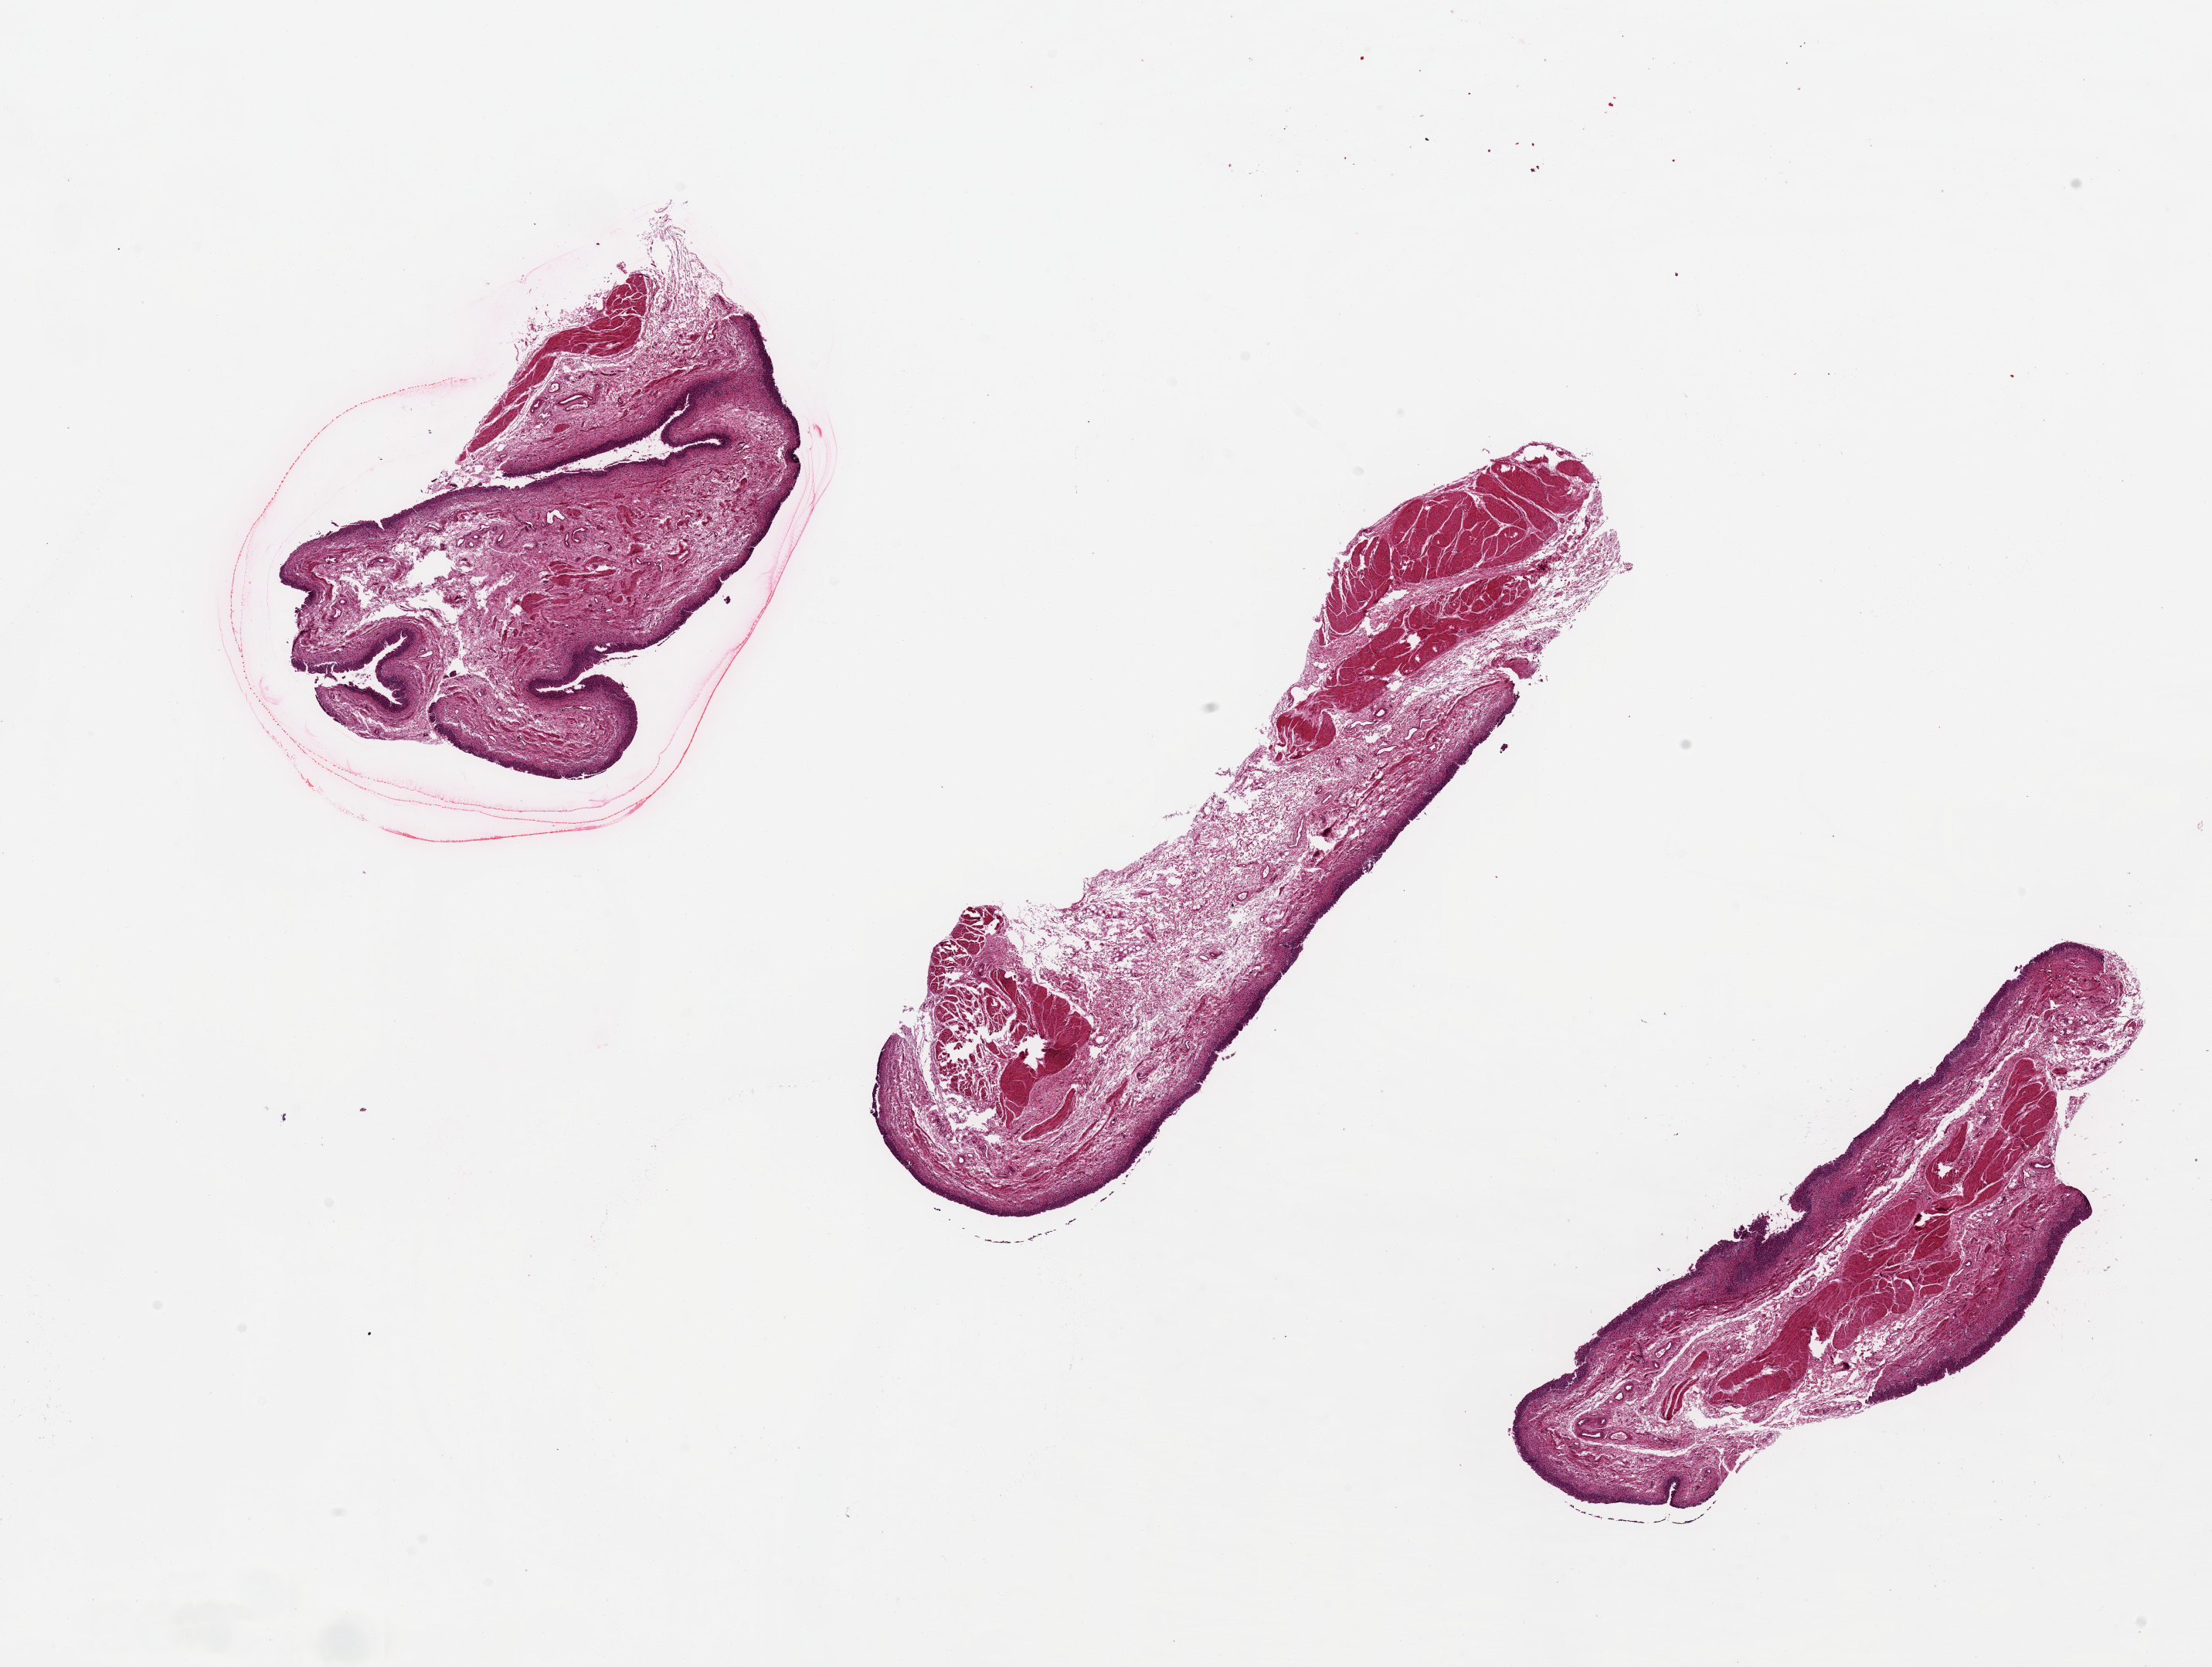
Digitized hematoxylin and eosin (H&E)-stained section — whole scanned area (about 22.6 x 17.1 mm) shown as a low-resolution overview. PAXgene-fixed, paraffin-embedded tissue. Target tissue: urinary bladder. Tissue donor sample. Donor sex: female.
• review note (as recorded): 3 ~9x2m pieces. Urothelium fairly well preserved; 4-5% of thickness. Areas of poor fixation